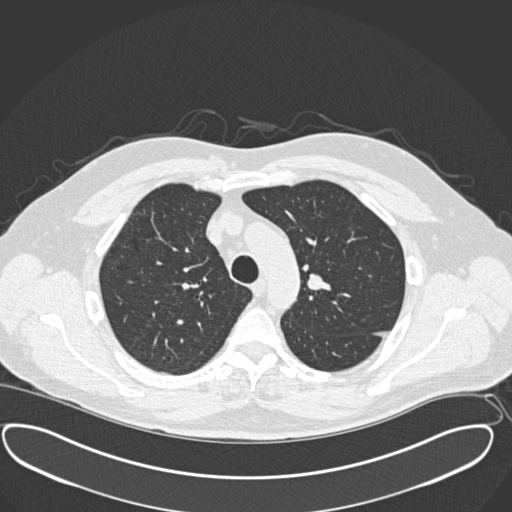
Low-dose screening chest CT, axial slice, third screening round (two years after baseline), lung window (W 1500 / L -600 HU), 2 mm slice thickness, slice 48 of 181 in the series. Male participant, aged 56 years at enrolment. Current smoker at enrolment.
Lesion marked by an expert reader, box from (x=288, y=262) to (x=344, y=309) px. No non-calcified nodule or mass ≥4 mm was recorded by the screening reader at this exam. Lung cancer was diagnosed 156 days after this screen: neuroendocrine carcinoma, NOS, left upper lobe, well differentiated (G1), stage IA (AJCC 6th edition), 20 mm at pathology.